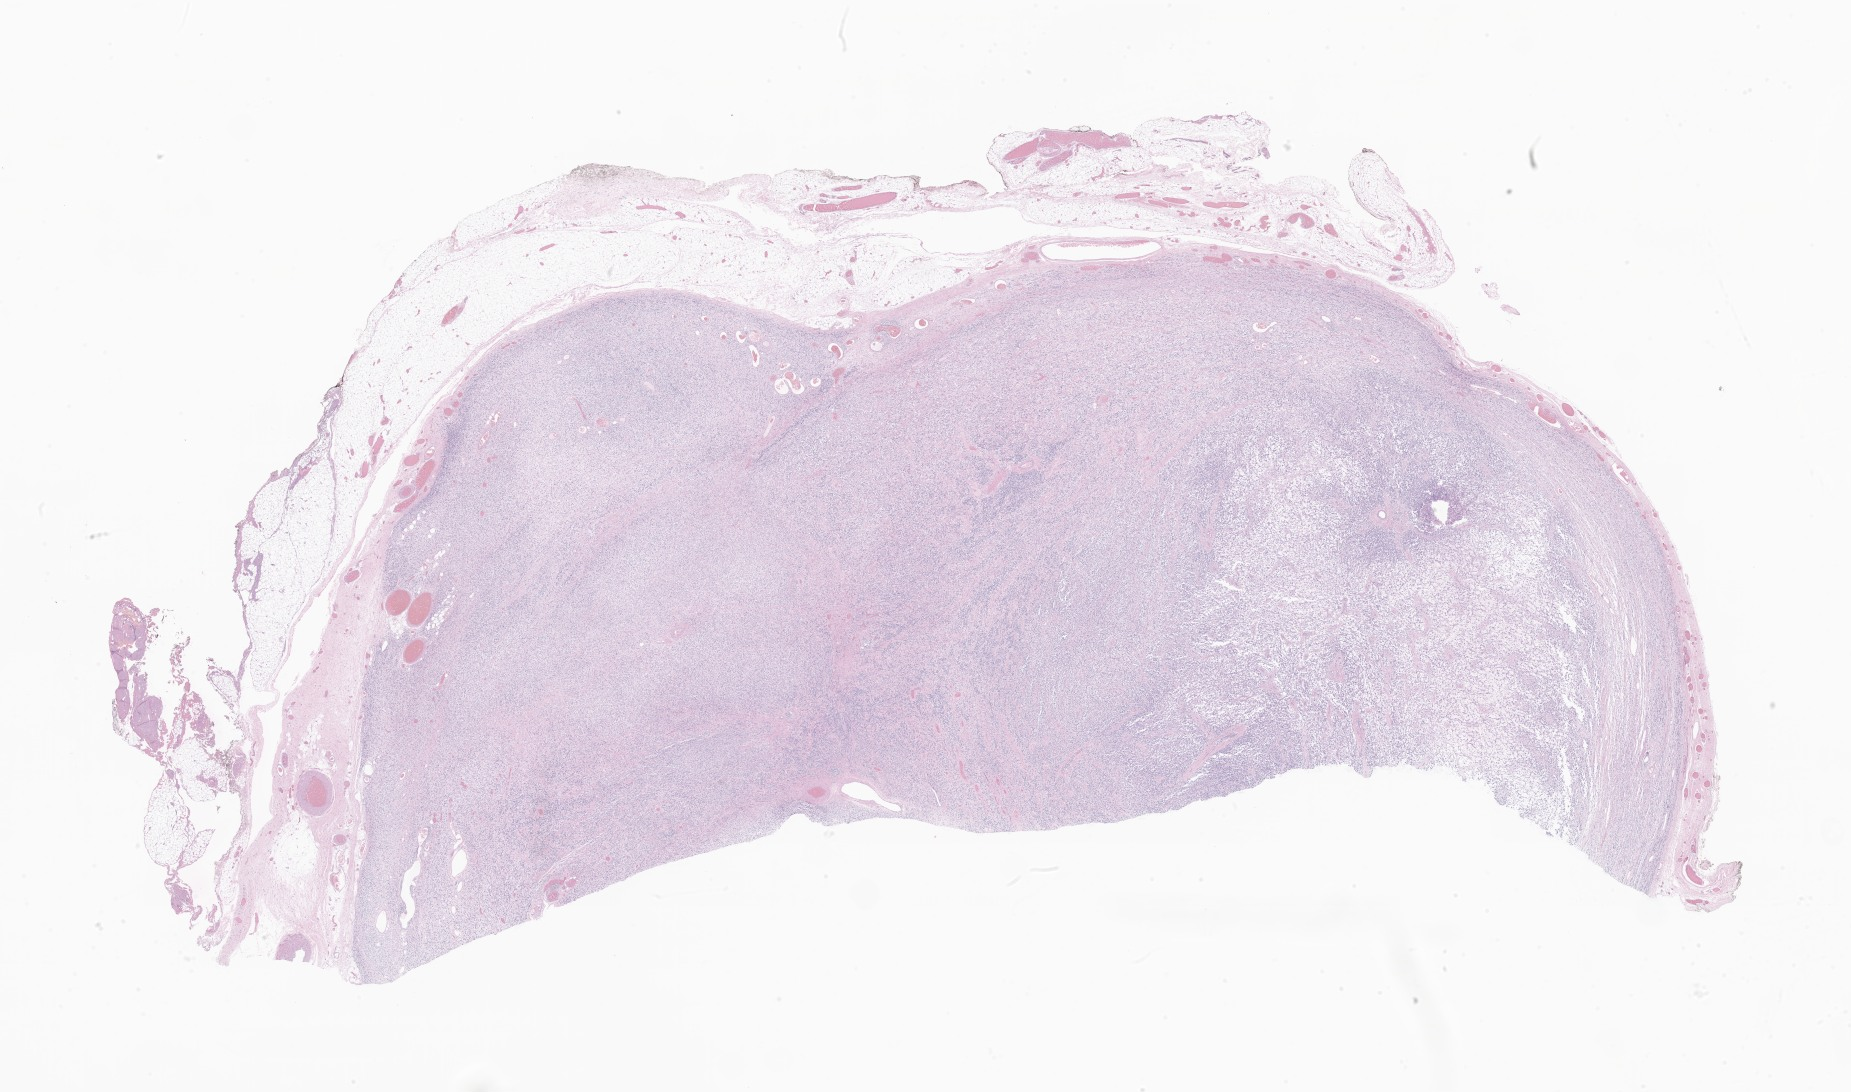
Whole-slide image, hematoxylin and eosin (H&E) stain of tumor tissue from the testis — whole scanned area (about 31.2 x 18.4 mm) shown as a low-resolution overview; formalin-fixed, paraffin-embedded (FFPE) tissue. Patient male; age 187 months (15 years 7 months).
Recorded diagnosis: Genital rhabdomyoma.